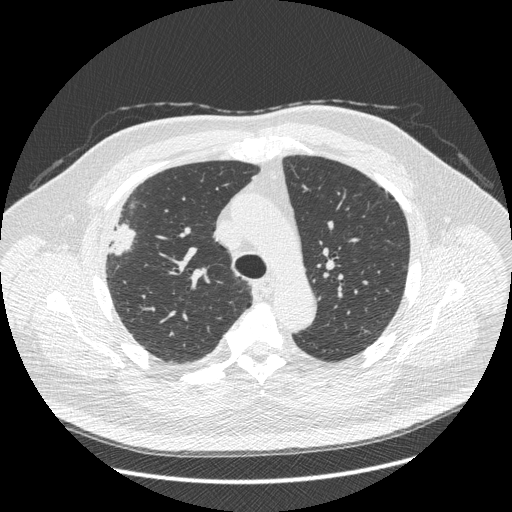
Low-dose screening chest CT, one axial slice; lung window (W 1500 / L -600 HU); 1.25 mm slice thickness; 512 × 512 image matrix, field of view 400 × 400 mm.
Structures marked on this image (outlined manually by an expert reader):
- lesion 1 (tumor, upper lobe of right lung): bounding box [x1, y1, x2, y2] px = [110, 224, 136, 255]